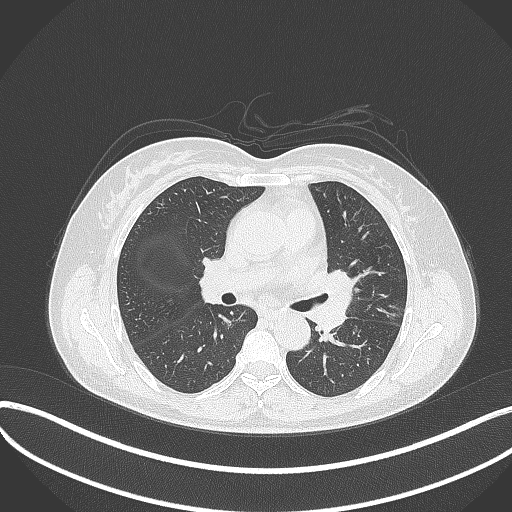
Chest CT, one axial slice. Position 198 of 373 along the scan axis. Reconstruction kernel B70f. Lung window (W 1500 / L -600 HU). 1 mm slice thickness. 512 × 512 image matrix, field of view 400 × 400 mm. Female patient, age 54 years. From the clinical record (not read from this slice): clinical TNM (as recorded): T2a N1 M0; histopathological grade: G3.
Outlined on this slice (bounding box drawn by a radiologist):
- lung tumour (recorded histology: small cell carcinoma): bounding box (x1, y1, x2, y2) in pixels: (316, 264, 356, 336)